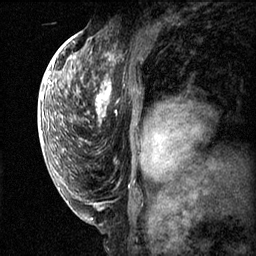
Breast MRI (dynamic contrast-enhanced), one sagittal slice; position 37 of 60 along the scan axis; dynamic contrast-enhanced series, image 2 of 3 at this slice position (ordered by acquisition); 1.5 T; TE 4.2 ms, TR 11.1 ms; 2 mm slice thickness; 256 × 256 image matrix, field of view 180 × 180 mm. Female patient, age 50 years.
Structures marked on this image (semi-automatically segmented with operator editing):
- analysis volume of interest (the breast-tissue region the enhancement analysis was run in; not a lesion): bounding box [x1, y1, x2, y2] px = [82, 56, 162, 143]
- tumour enhancement mask (voxels above the 70 % enhancement threshold inside the analysis volume of interest): [97, 86, 154, 143]